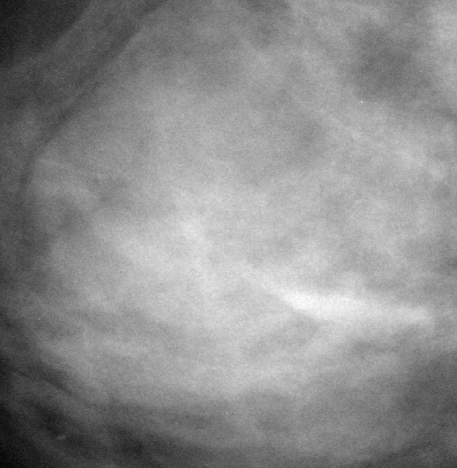
Region of interest cut from a scanned film mammogram (one marked finding), right breast, MLO view.
Finding: mass, shape lobulated, margins circumscribed; BI-RADS assessment category 4; subtlety rating 4 on a 1 (subtle) to 5 (obvious) scale; pathology result (as recorded, not read from the image): benign.